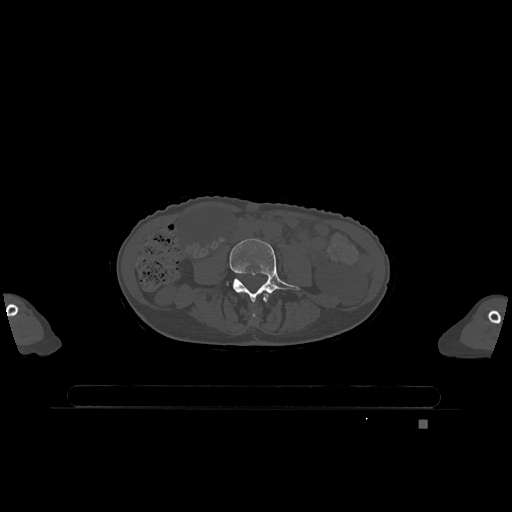
CT including the spine, one axial slice. Slice 301 of 1317 in the series (ordered by position). Bone window (W 1800 / L 400 HU). 512 × 512 image matrix. Patient: female, 74 years. Case-level facts recorded for this patient, not image findings: primary cancer: lung; vertebrae with lytic lesions (as recorded): T1, T4, T5, T6, L4, L5.
Structures marked on this image (semi-automatic segmentation, software-assisted and operator-edited):
- L3 vertebra: bounding box <246,292,270,318> (left, top, right, bottom; pixels)
- L4 vertebra: <226,239,300,302>